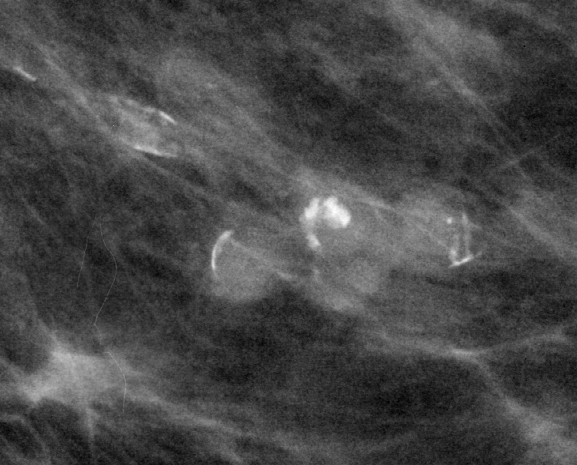
Region of interest cut from a scanned film mammogram (one marked finding); left breast; MLO view.
Finding: calcifications, morphology eggshell, distribution segmental; BI-RADS assessment category 2; benign without callback (not worked up further).